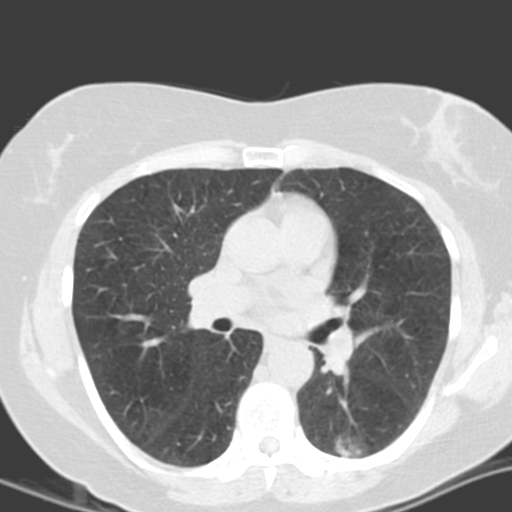
Chest CT (low-dose screening protocol), one axial image. Second screening round (one year after baseline). Lung window (W 1500 / L -600 HU). Slice 64 of 161 in the series. 512 × 512 image matrix, field of view 290 × 290 mm. Female participant, aged 55 years at enrolment.
• Expert reader's lesion annotation, bounding box (x1, y1, x2, y2) in pixels: (304, 409, 381, 472).
• The screening reader recorded 4 non-calcified nodules or masses ≥4 mm on this exam; which of them this box marks is not recorded.